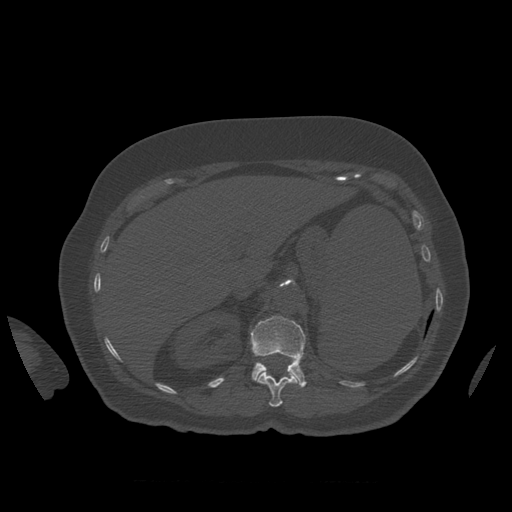
CT including the spine, one axial slice; slice 289 of 399 in the series (ordered by position); reconstruction kernel STANDARD; 120 kVp; bone window (W 1800 / L 400 HU); 1.25 mm slice thickness; 512 × 512 image matrix, field of view 404 × 404 mm. Patient age 81 years. Case-level facts recorded for this patient, not image findings: primary cancer: renal.
Structures marked on this image (semi-automatic segmentation, software-assisted and operator-edited):
- L1 vertebra: bounding box <251,316,307,388> (left, top, right, bottom; pixels)
- T12 vertebra: <257,372,297,407>